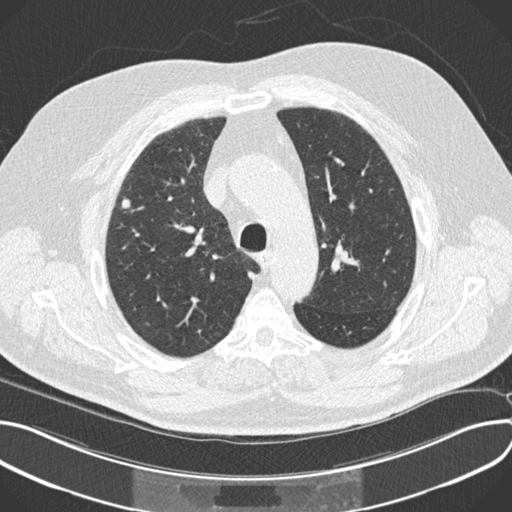
Low-dose screening chest CT, one axial slice; slice 158 of 212 in the series (ordered by position); reconstruction kernel B30f; lung window (W 1500 / L -600 HU); 2 mm slice thickness; 512 × 512 image matrix, field of view 380 × 380 mm.
Outlined on this slice (expert manual segmentation):
- lesion 1 (tumor, upper lobe of right lung): box from (x=122, y=199) to (x=131, y=209) px